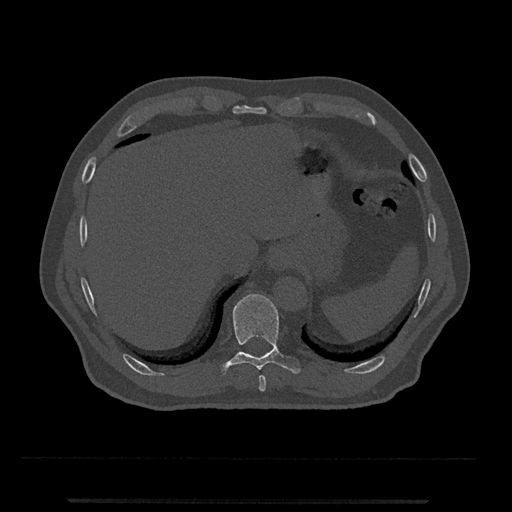
CT including the spine, one axial slice; slice 520 of 797 in the series (ordered by position); reconstruction kernel Br40s/3; bone window (W 1800 / L 400 HU); 0.5 mm slice thickness; 512 × 512 image matrix. Patient: male, 63 years. Case-level facts recorded for this patient, not image findings: primary cancer: prostate.
Annotated regions visible in this slice (semi-automatic segmentation, software-assisted and operator-edited):
- T10 vertebra: box from (x=220, y=294) to (x=301, y=375) px
- T9 vertebra: (x=259, y=375)–(x=266, y=392)